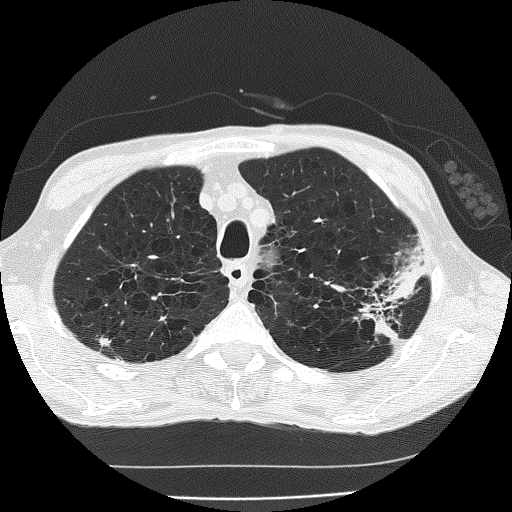
Axial slice from a low-dose chest CT screening exam; second screening round (one year after baseline); lung window (W 1500 / L -600 HU); 2 mm slice thickness; lung (sharp) reconstruction kernel (FC51); 120 kVp; slice 38 of 185 in the series; 512 × 512 image matrix. Male participant, aged 60 years at enrolment. Current smoker at enrolment.
Expert reader's lesion annotation, bounding box [x1, y1, x2, y2] px = [346, 258, 429, 339]. The screening reader recorded 2 non-calcified nodules or masses ≥4 mm on this exam; which of them this box marks is not recorded. Official screen result: positive, other.